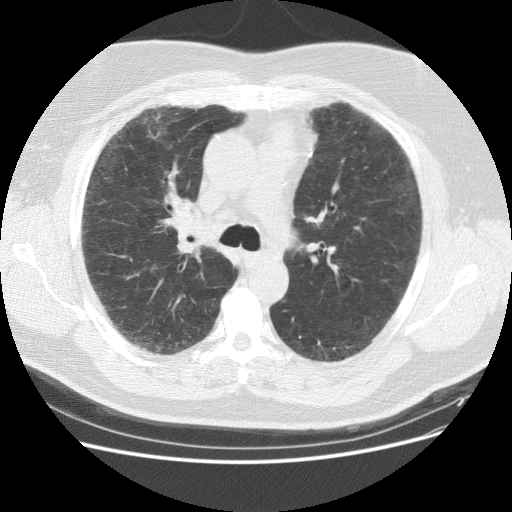
Axial slice from a low-dose chest CT screening exam, first (baseline) screen, lung window (W 1500 / L -600 HU), 2.5 mm slice thickness, 120 kVp, slice 46 of 151 in the series. Male participant, aged 59 years at enrolment.
Lesion marked by an expert reader, bounding box <161,201,204,240> (left, top, right, bottom; pixels). The screening reader recorded 2 non-calcified nodules or masses ≥4 mm on this exam (right middle lobe, right lower lobe); which of them this box marks is not recorded. Official screen result: positive, change unspecified: nodule(s) >= 4 mm or enlarging nodule(s), mass(es), or other non-specific abnormalities suspicious for lung cancer. Later outcome: lung cancer diagnosed 338 days after this screen — adenocarcinoma, NOS, right upper lobe, right middle lobe, moderately differentiated (G2), stage IA (AJCC 6th edition), 13 mm at pathology.